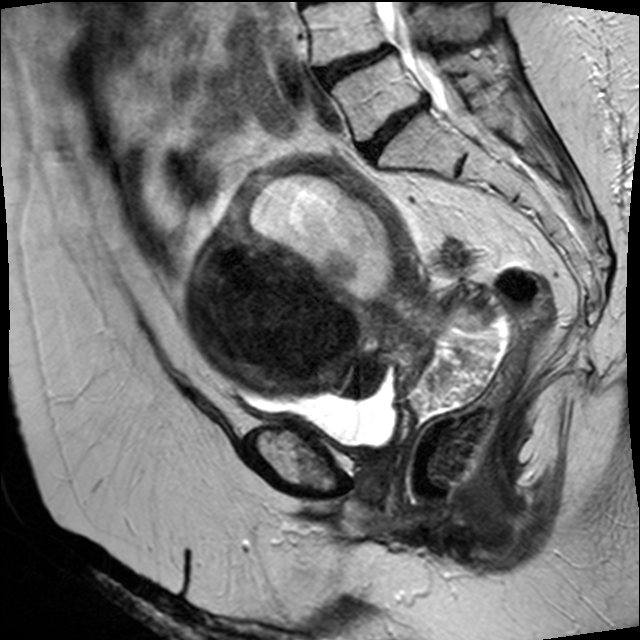
Pelvic MRI for cervical cancer, one sagittal slice; T2-weighted; 1.5 T; TE 89 ms, TR 4610 ms; 4 mm slice thickness; 640 × 640 image matrix, field of view 260 × 260 mm. Patient: female, 50 years.
Structures marked on this image (manually delineated by an expert):
- uterus and cervix: box from (x=181, y=154) to (x=502, y=411) px